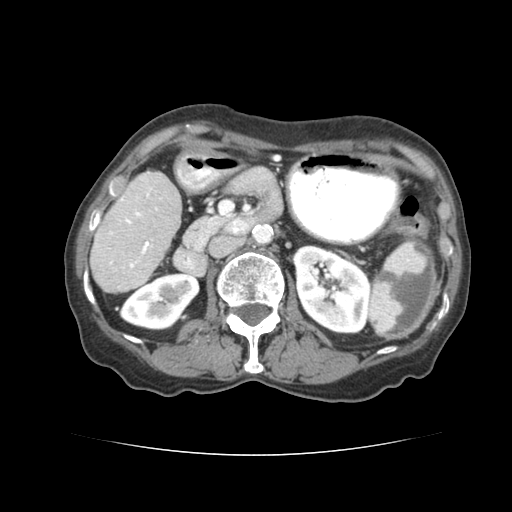
Contrast-enhanced abdominal CT (liver protocol), one axial slice; position 23 of 77 along the scan axis; soft-tissue window (W 400 / L 40 HU); 2.5 mm slice thickness; 512 × 512 image matrix. From the clinical record (not read from this slice): diagnosis: hepatocellular carcinoma (patient treated with transarterial chemoembolisation; whether this scan precedes or follows treatment is not stated here); TNM stage (as recorded): Stage-I.
Annotated regions visible in this slice (semi-automatically segmented with operator editing):
- liver parenchyma outside the tumour (the mass and vessels are separate outlines, so this box may not span the whole liver): bounding box <90,171,180,290> (left, top, right, bottom; pixels)
- liver vessels: <98,193,157,281>